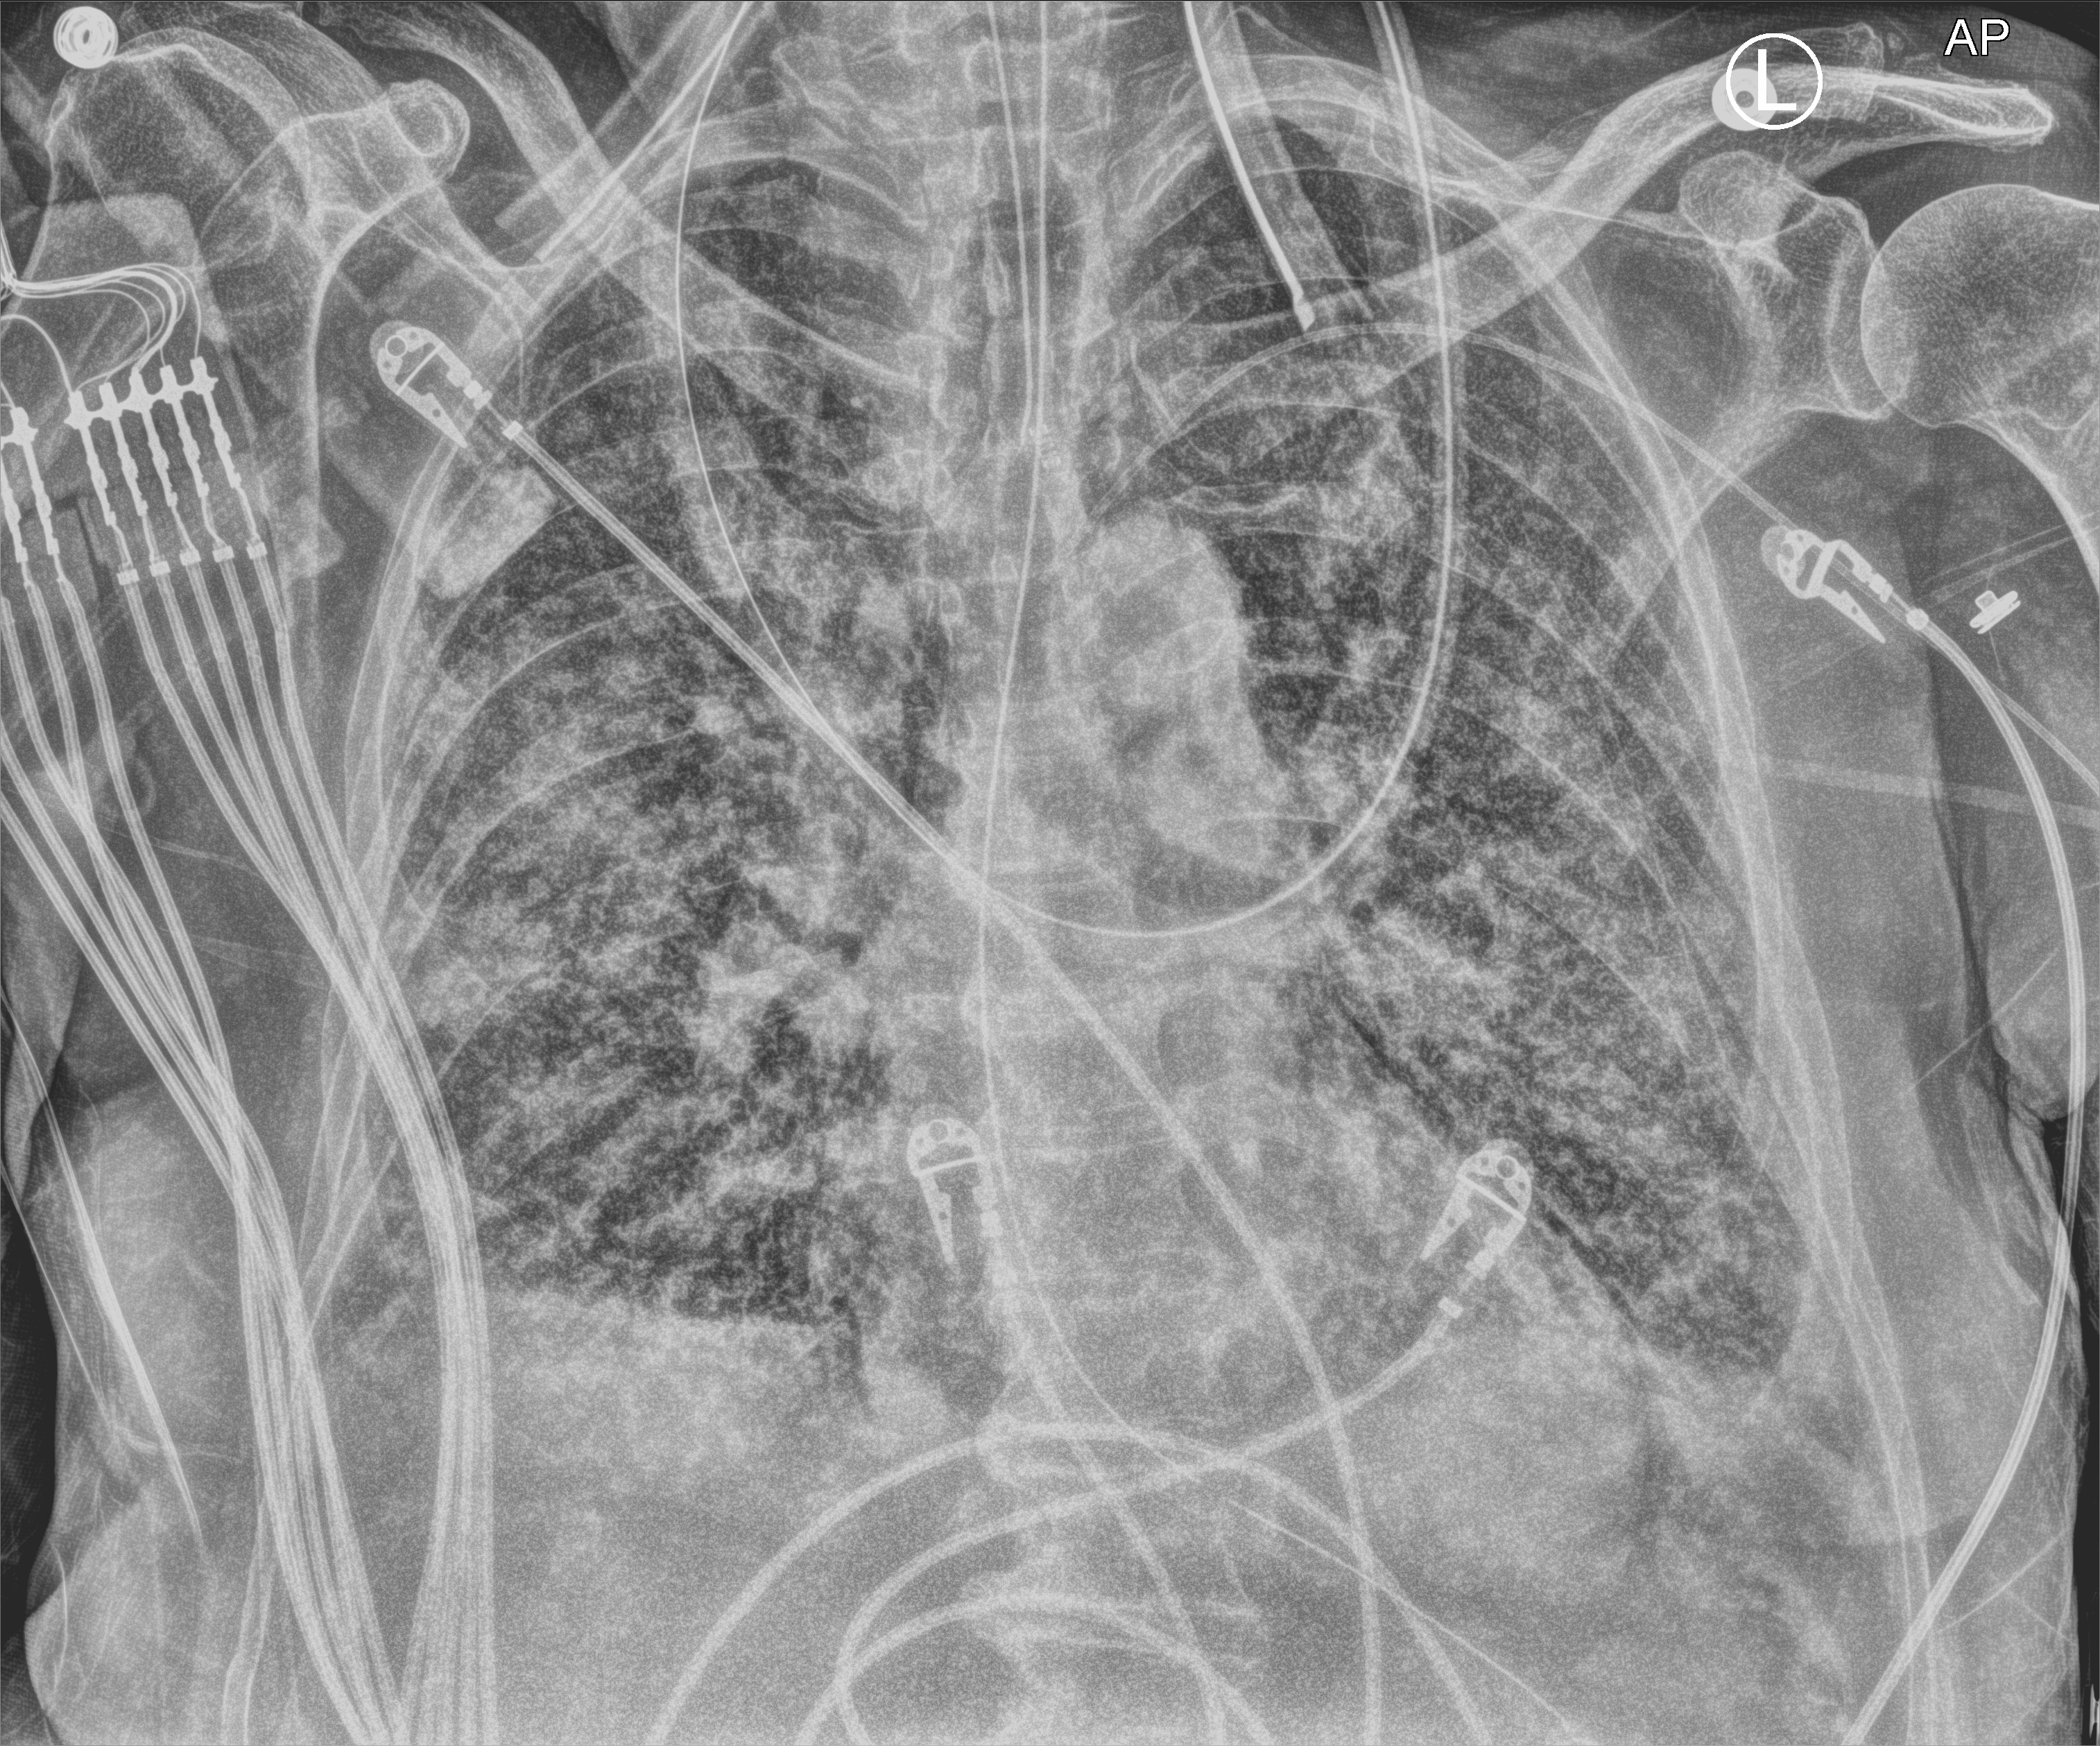
Chest X-ray (portable), anteroposterior (AP) projection. Patient hospitalised with COVID-19; male, aged 75–90 years.
From the hospital-stay record, not from the radiograph (when in the stay this image was taken is not recorded):
- mechanically ventilated during this hospital stay: yes
- admitted to intensive care during this hospital stay: yes
- hypertension (admission record): no